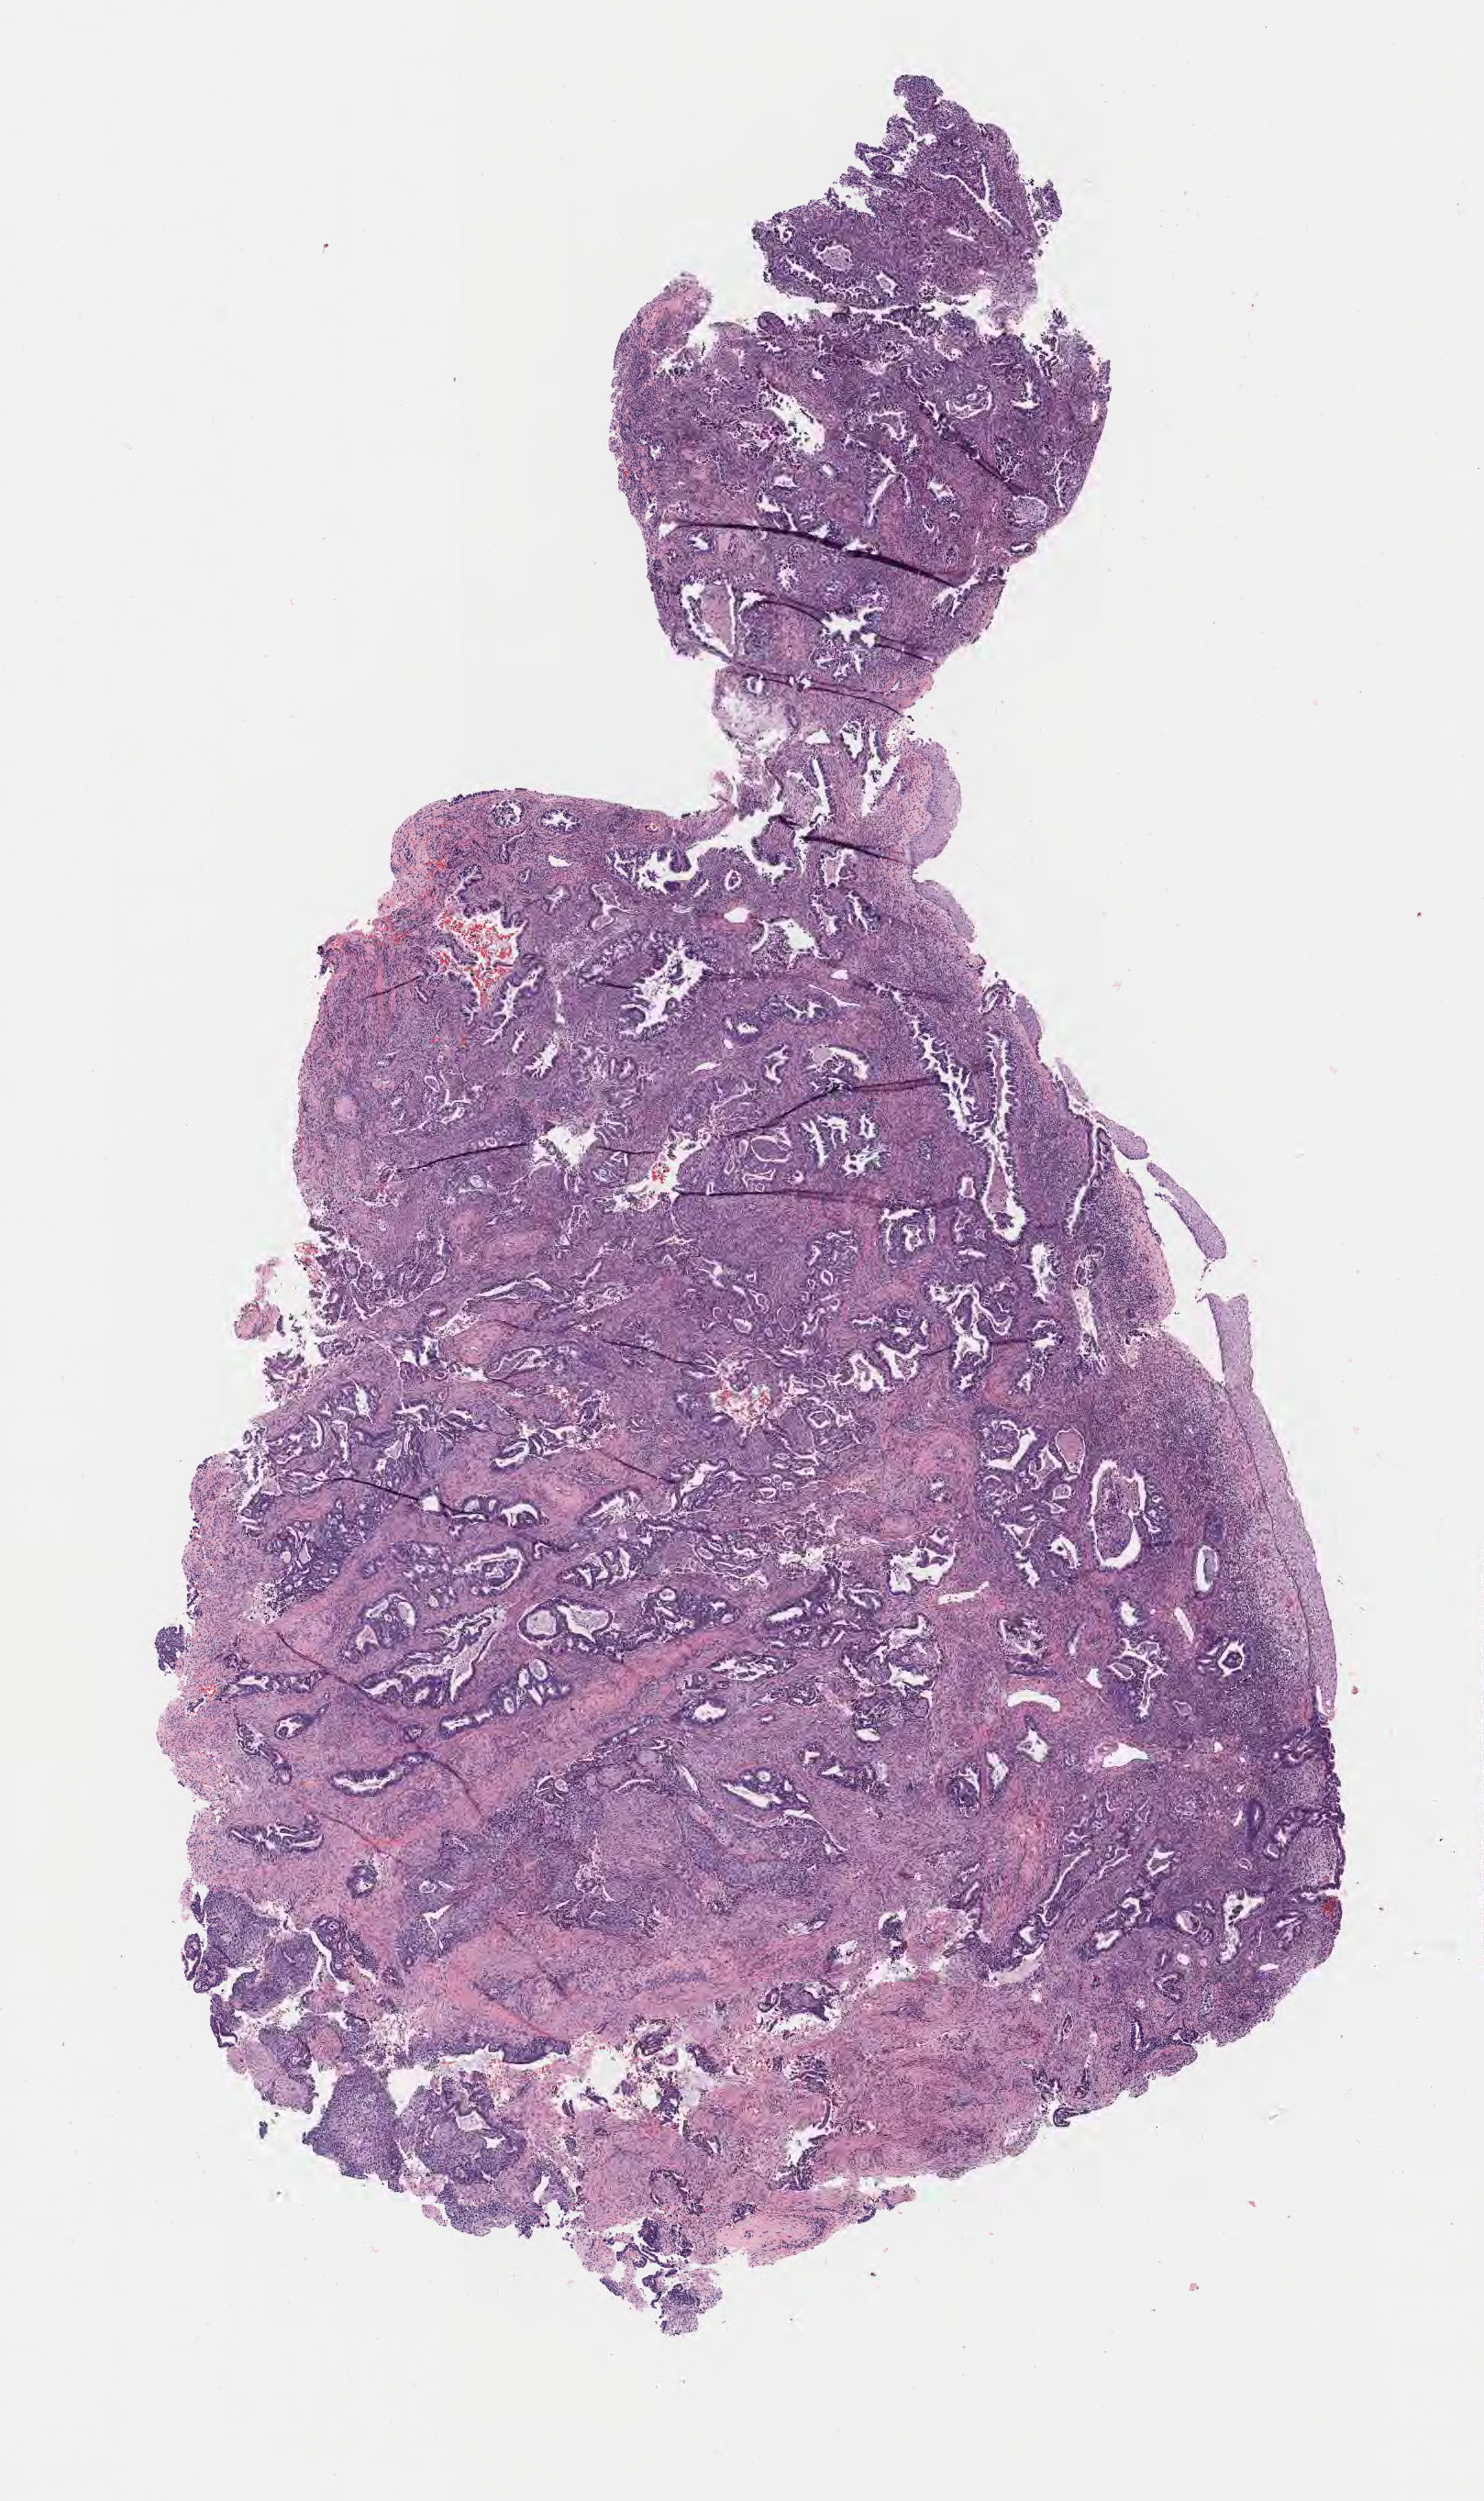
Whole-slide image, H&E stain — low-resolution overview of the scanned area, about 6.5 x 11.0 mm; specimen: tumor tissue; anatomic site: cervix. Patient female; age 56 years.
• histologic diagnosis: Adenosquamous carcinoma